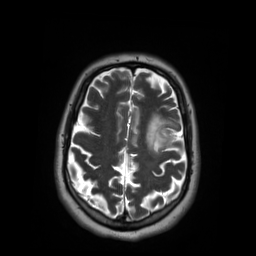
Brain MRI from a brain-tumour surgery series, one axial slice. Slice 41 of 59 in the series (ordered by position). 3.03 mm slice thickness. 256 × 256 image matrix, field of view 250 × 250 mm. From the clinical record (not read from this slice): histopathology: Oligodendroglioma; WHO grade: 2; IDH mutation: yes.
Structures marked on this image (expert manual segmentation):
- tumour: bounding box (x1, y1, x2, y2) in pixels: (145, 117, 178, 155)